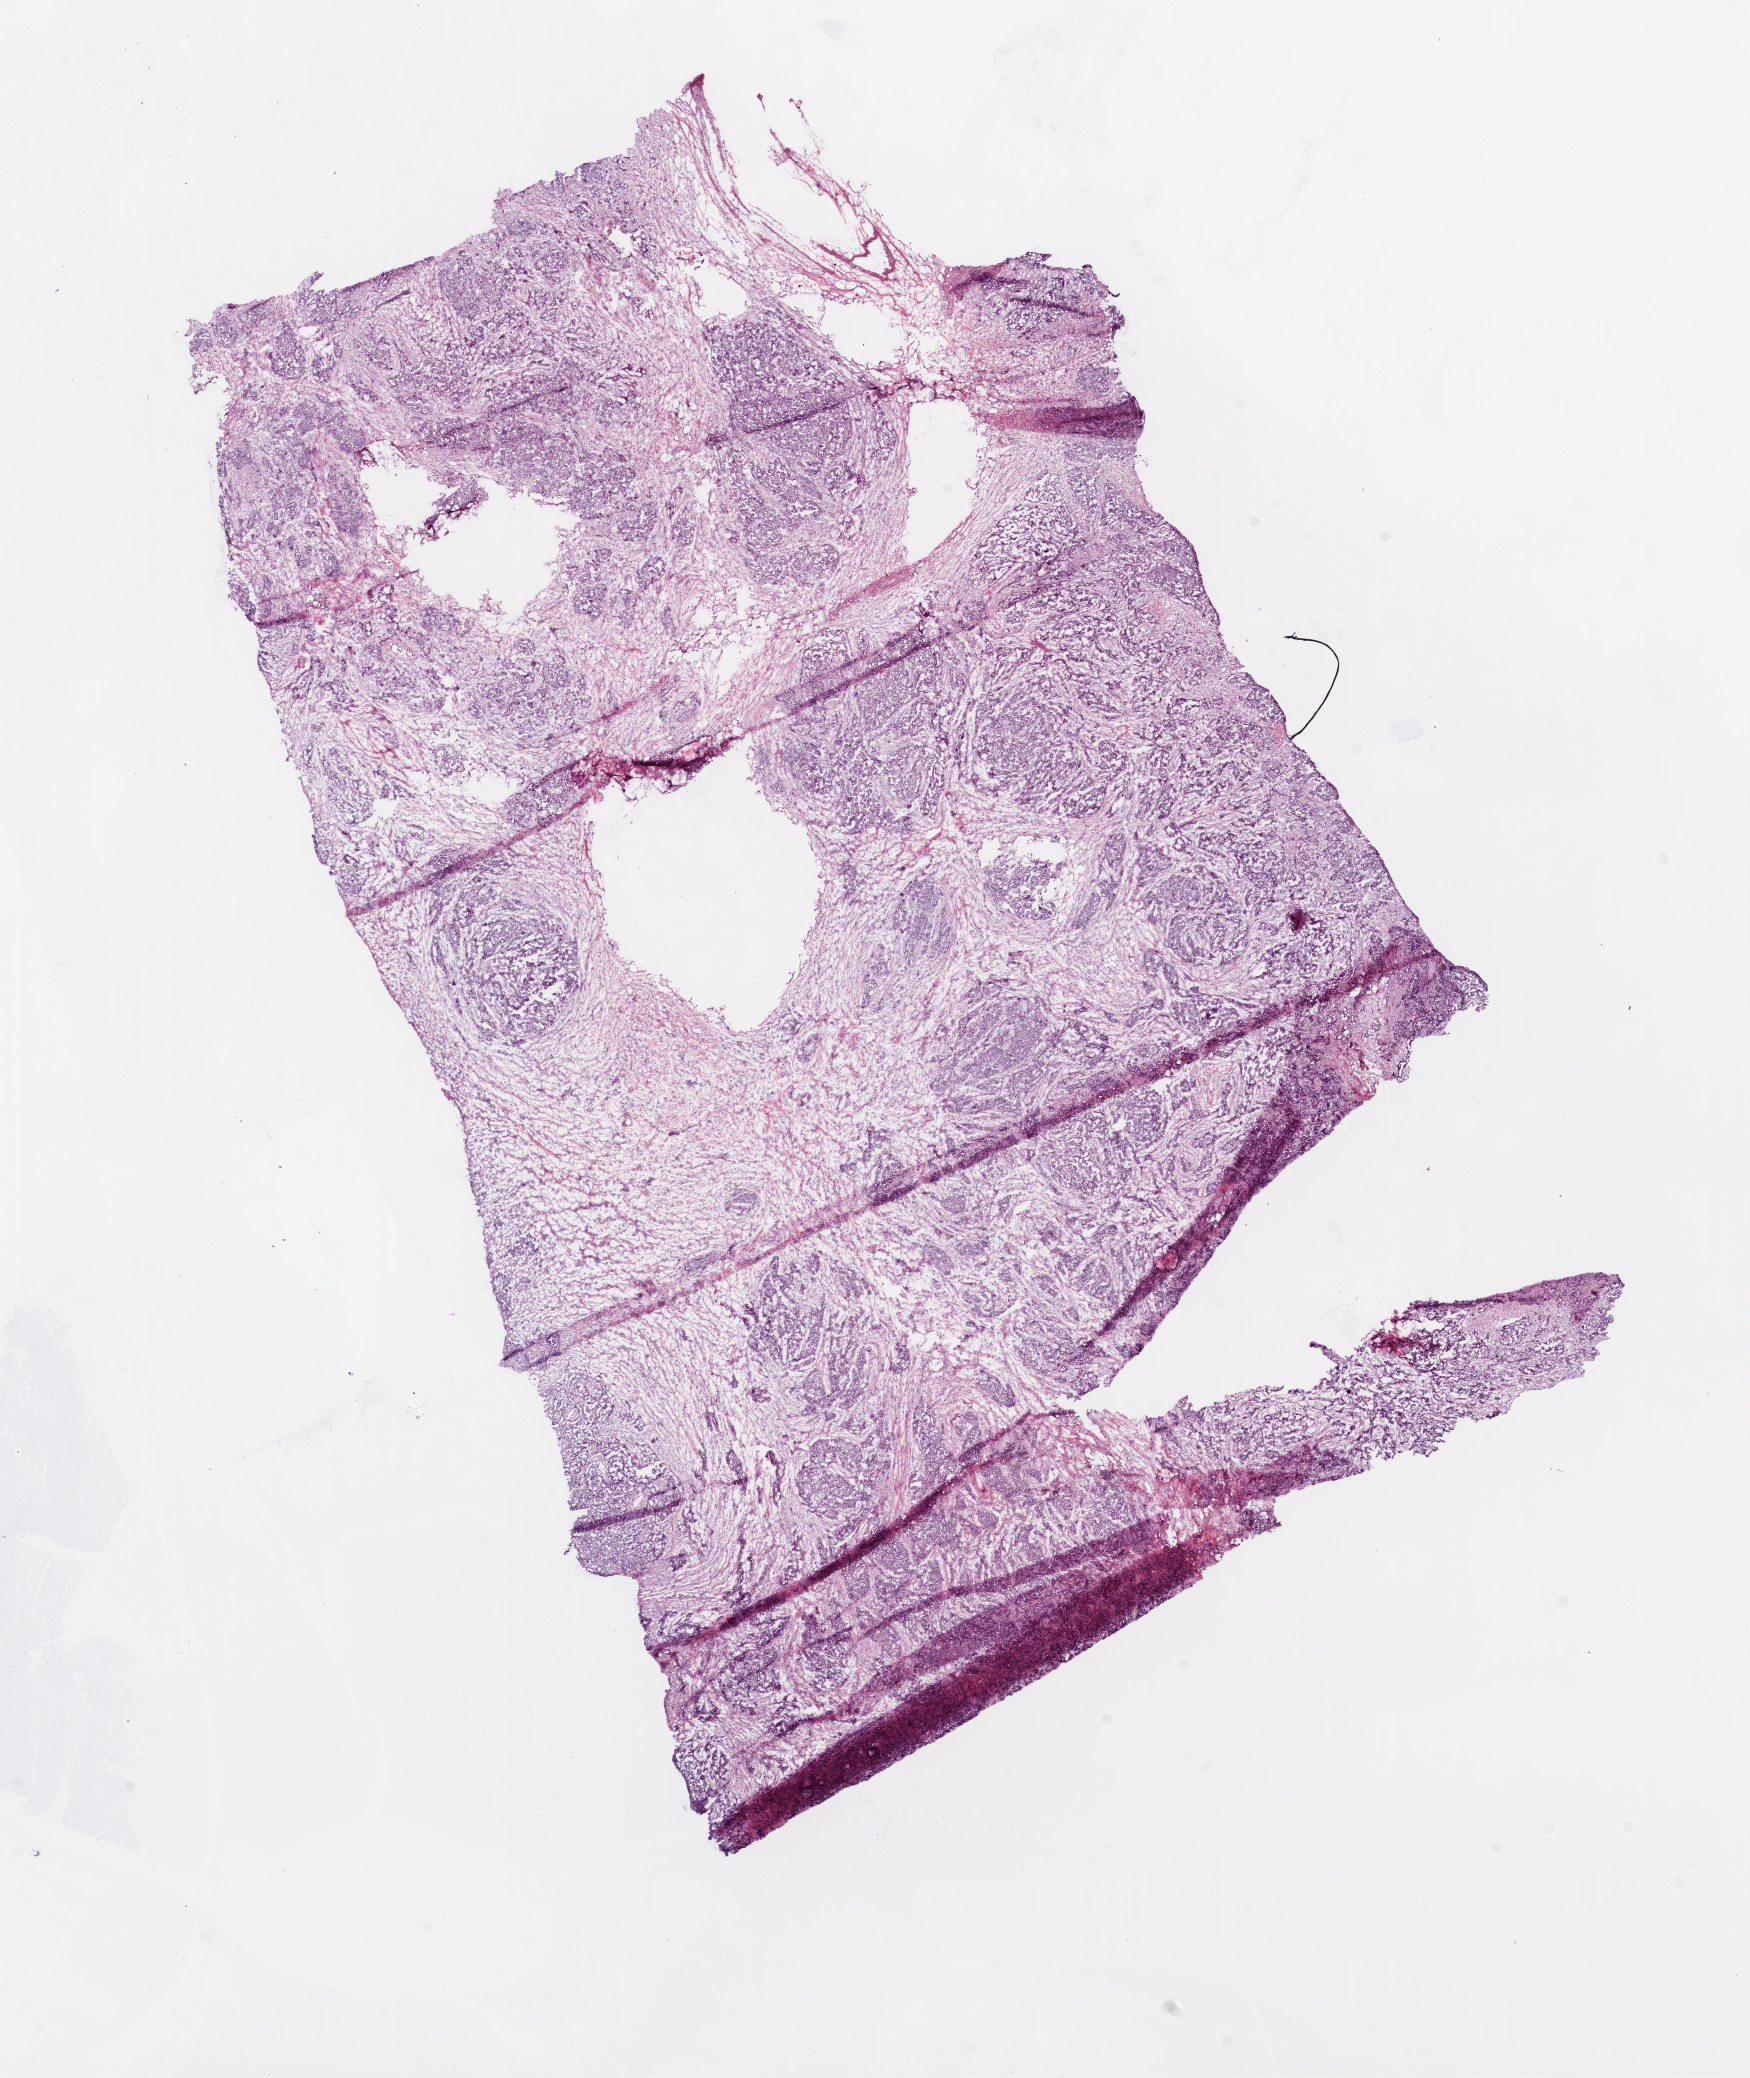
Digitized Hematoxylin and eosin (H&E) stained tissue section (whole slide), a low-resolution overview of the entire scanned area, about 14.0 x 16.7 mm; frozen section; sample: primary tumour, ovary. Female patient; age at initial diagnosis 63 years. Slide review estimates, as recorded: tumour cells 90%, tumour nuclei 90%.
Histologic diagnosis: Serous cystadenocarcinoma, NOS.